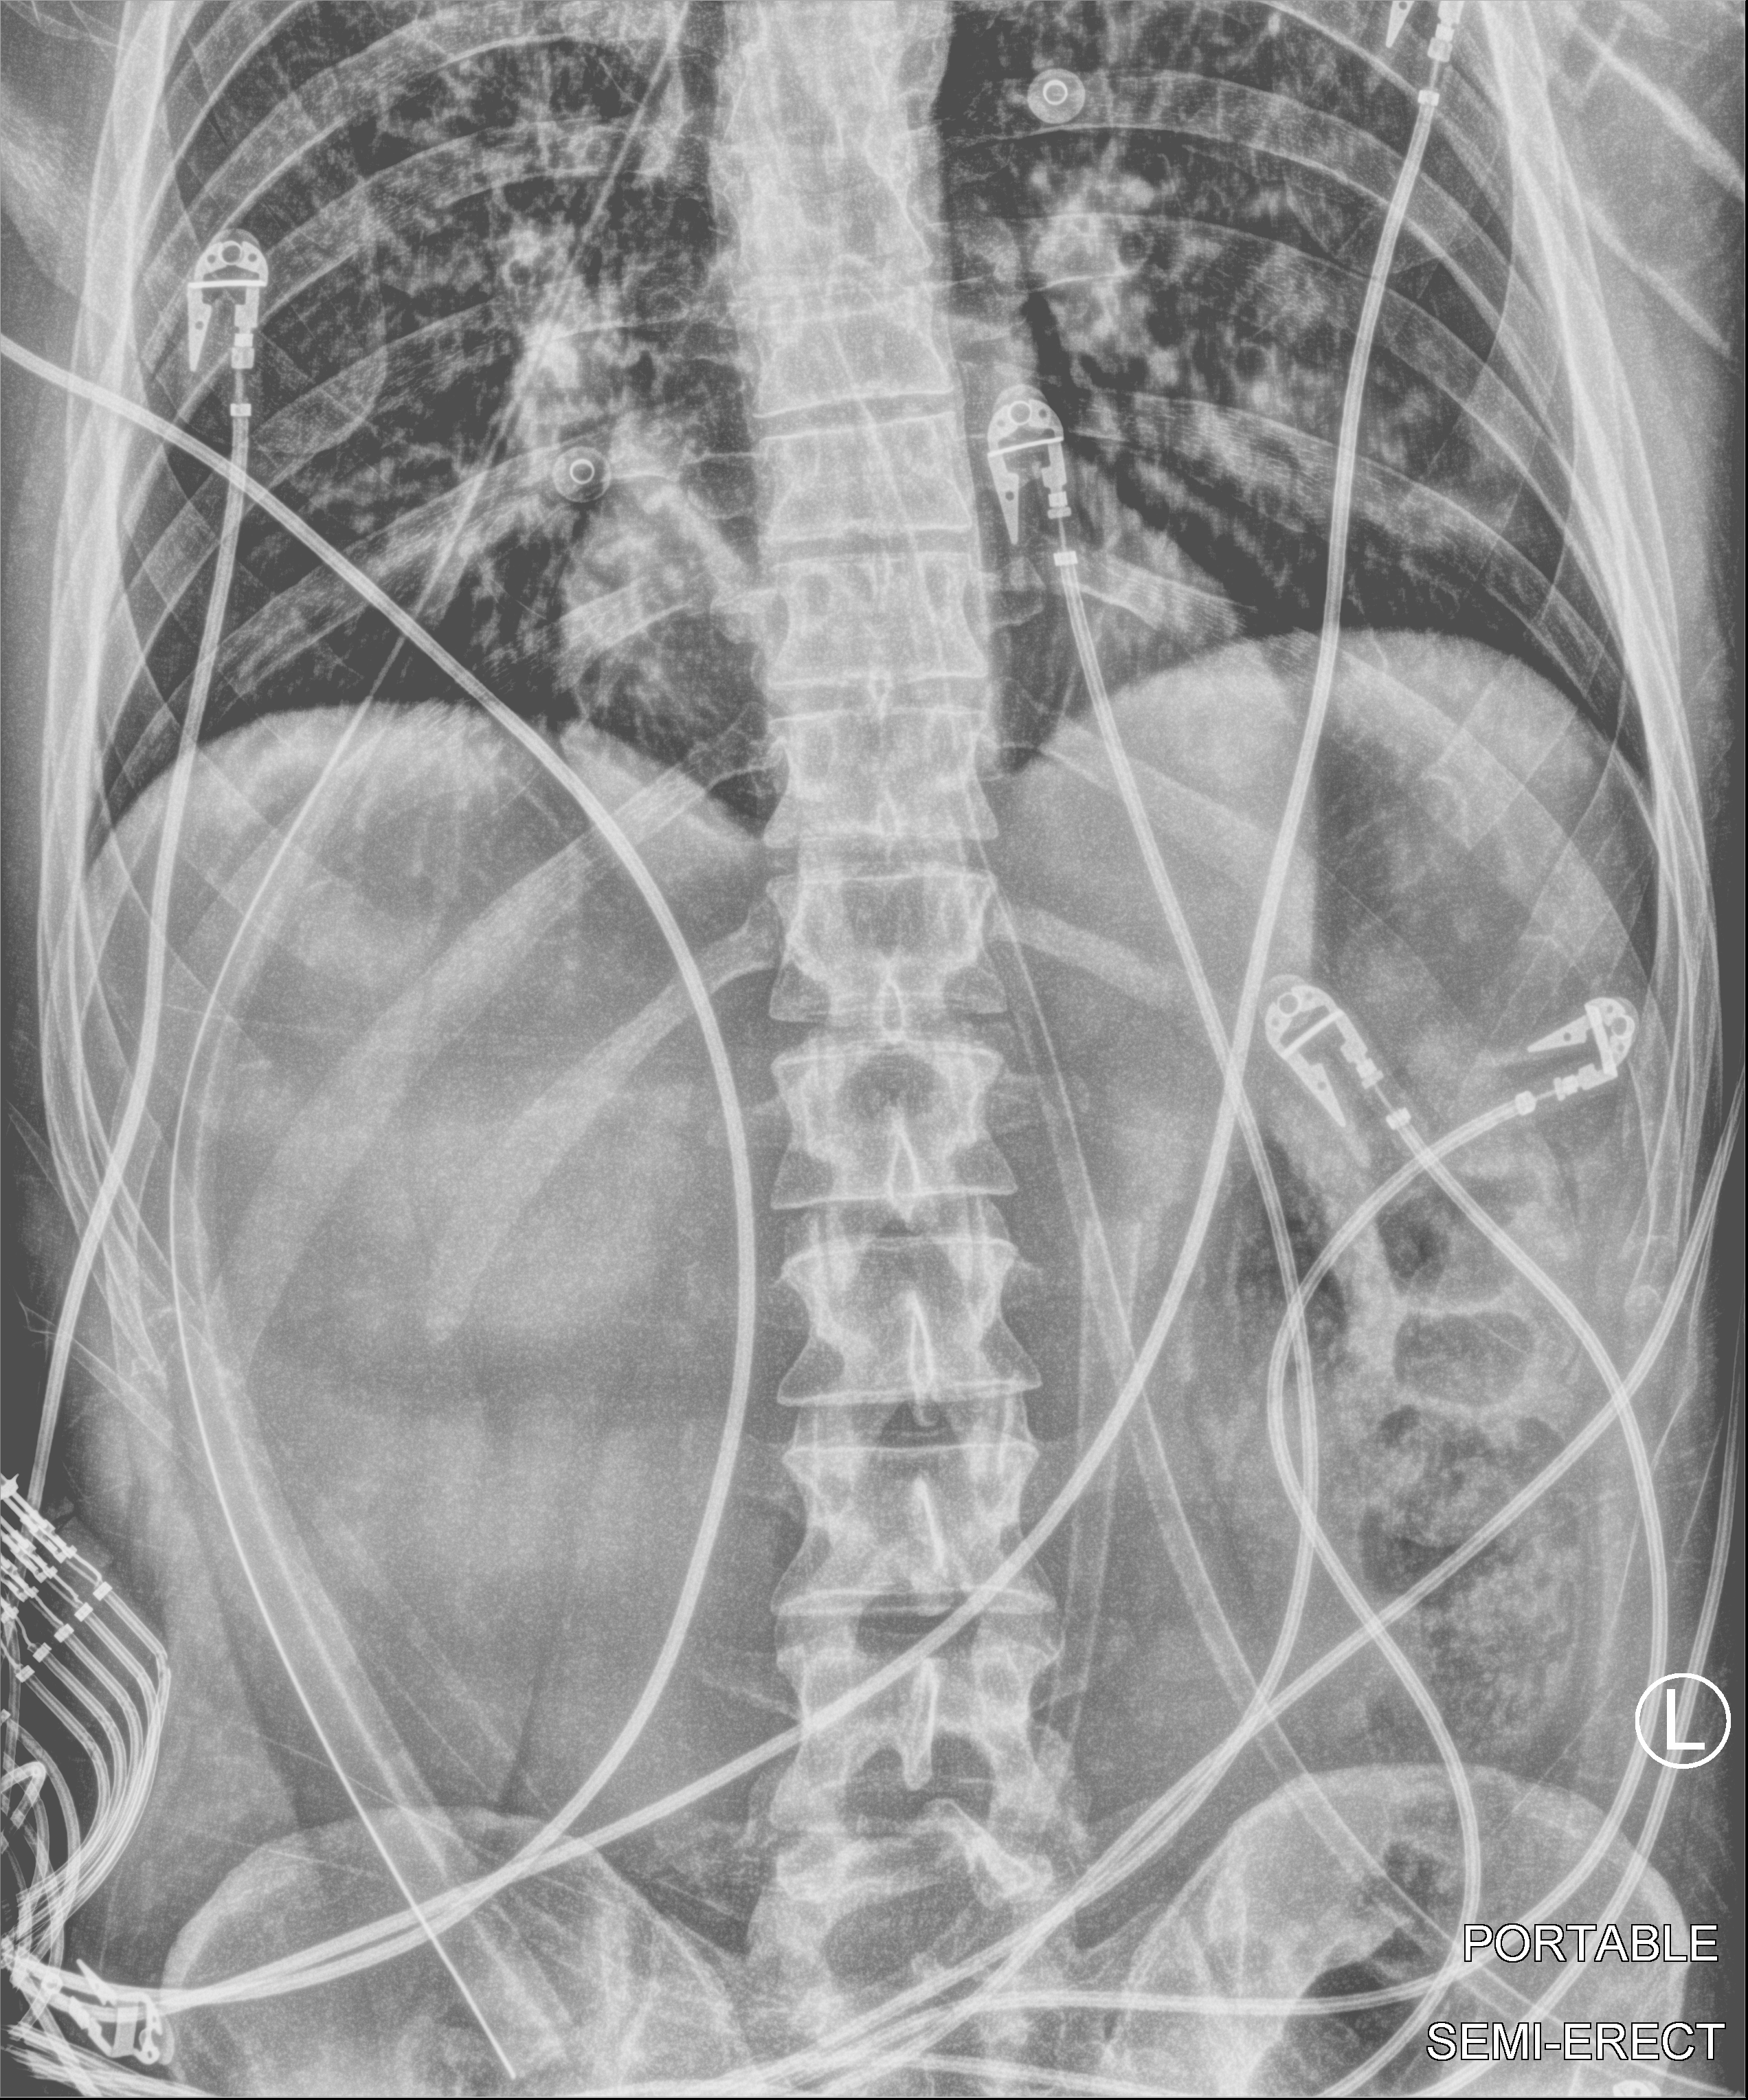
Bedside chest radiograph (computed radiography), anteroposterior (AP) projection. Patient hospitalised with COVID-19; male, aged 18–59 years.
From the hospital-stay record, not from the radiograph (when in the stay this image was taken is not recorded): admitted to intensive care during this hospital stay: no.